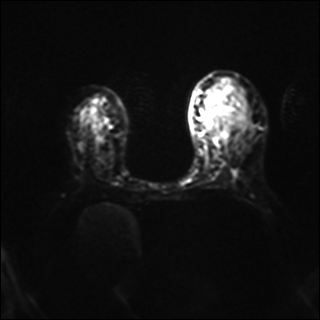
Breast MRI, one axial slice; slice 21 of 40 in the series (ordered by position); diffusion-weighted series; image 2 of 4 stored at this slice position (different b-values; order by instance number); 1.5 T; 4 mm slice thickness; 320 × 320 image matrix, field of view 320 × 320 mm. Female patient.
Structures marked on this image (outlined manually by an expert reader):
- tumour on diffusion-weighted imaging: bounding box [x1, y1, x2, y2] px = [220, 98, 239, 123]